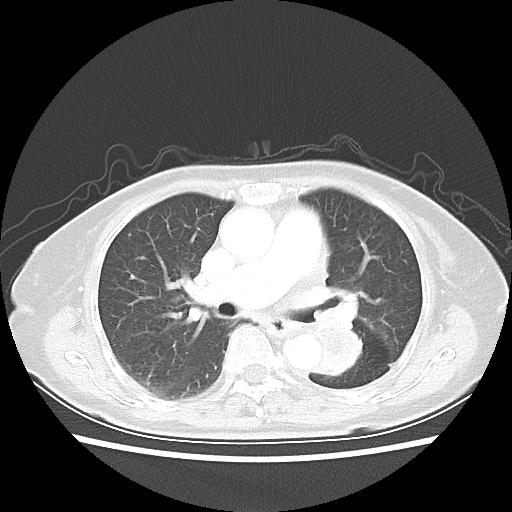
Chest CT, one axial slice. Position 29 of 50 along the scan axis. Reconstruction kernel LUNG. Lung window (W 1500 / L -600 HU). 5 mm slice thickness. 512 × 512 image matrix, field of view 335 × 335 mm. Female patient, age 81 years. From the clinical record (not read from this slice): clinical TNM (as recorded): T2 N0 M1a.
Annotated regions visible in this slice (rectangle marked by the reading radiologist):
- lung tumour (recorded histology: squamous cell carcinoma): bounding box (x1, y1, x2, y2) in pixels: (301, 310, 368, 383)